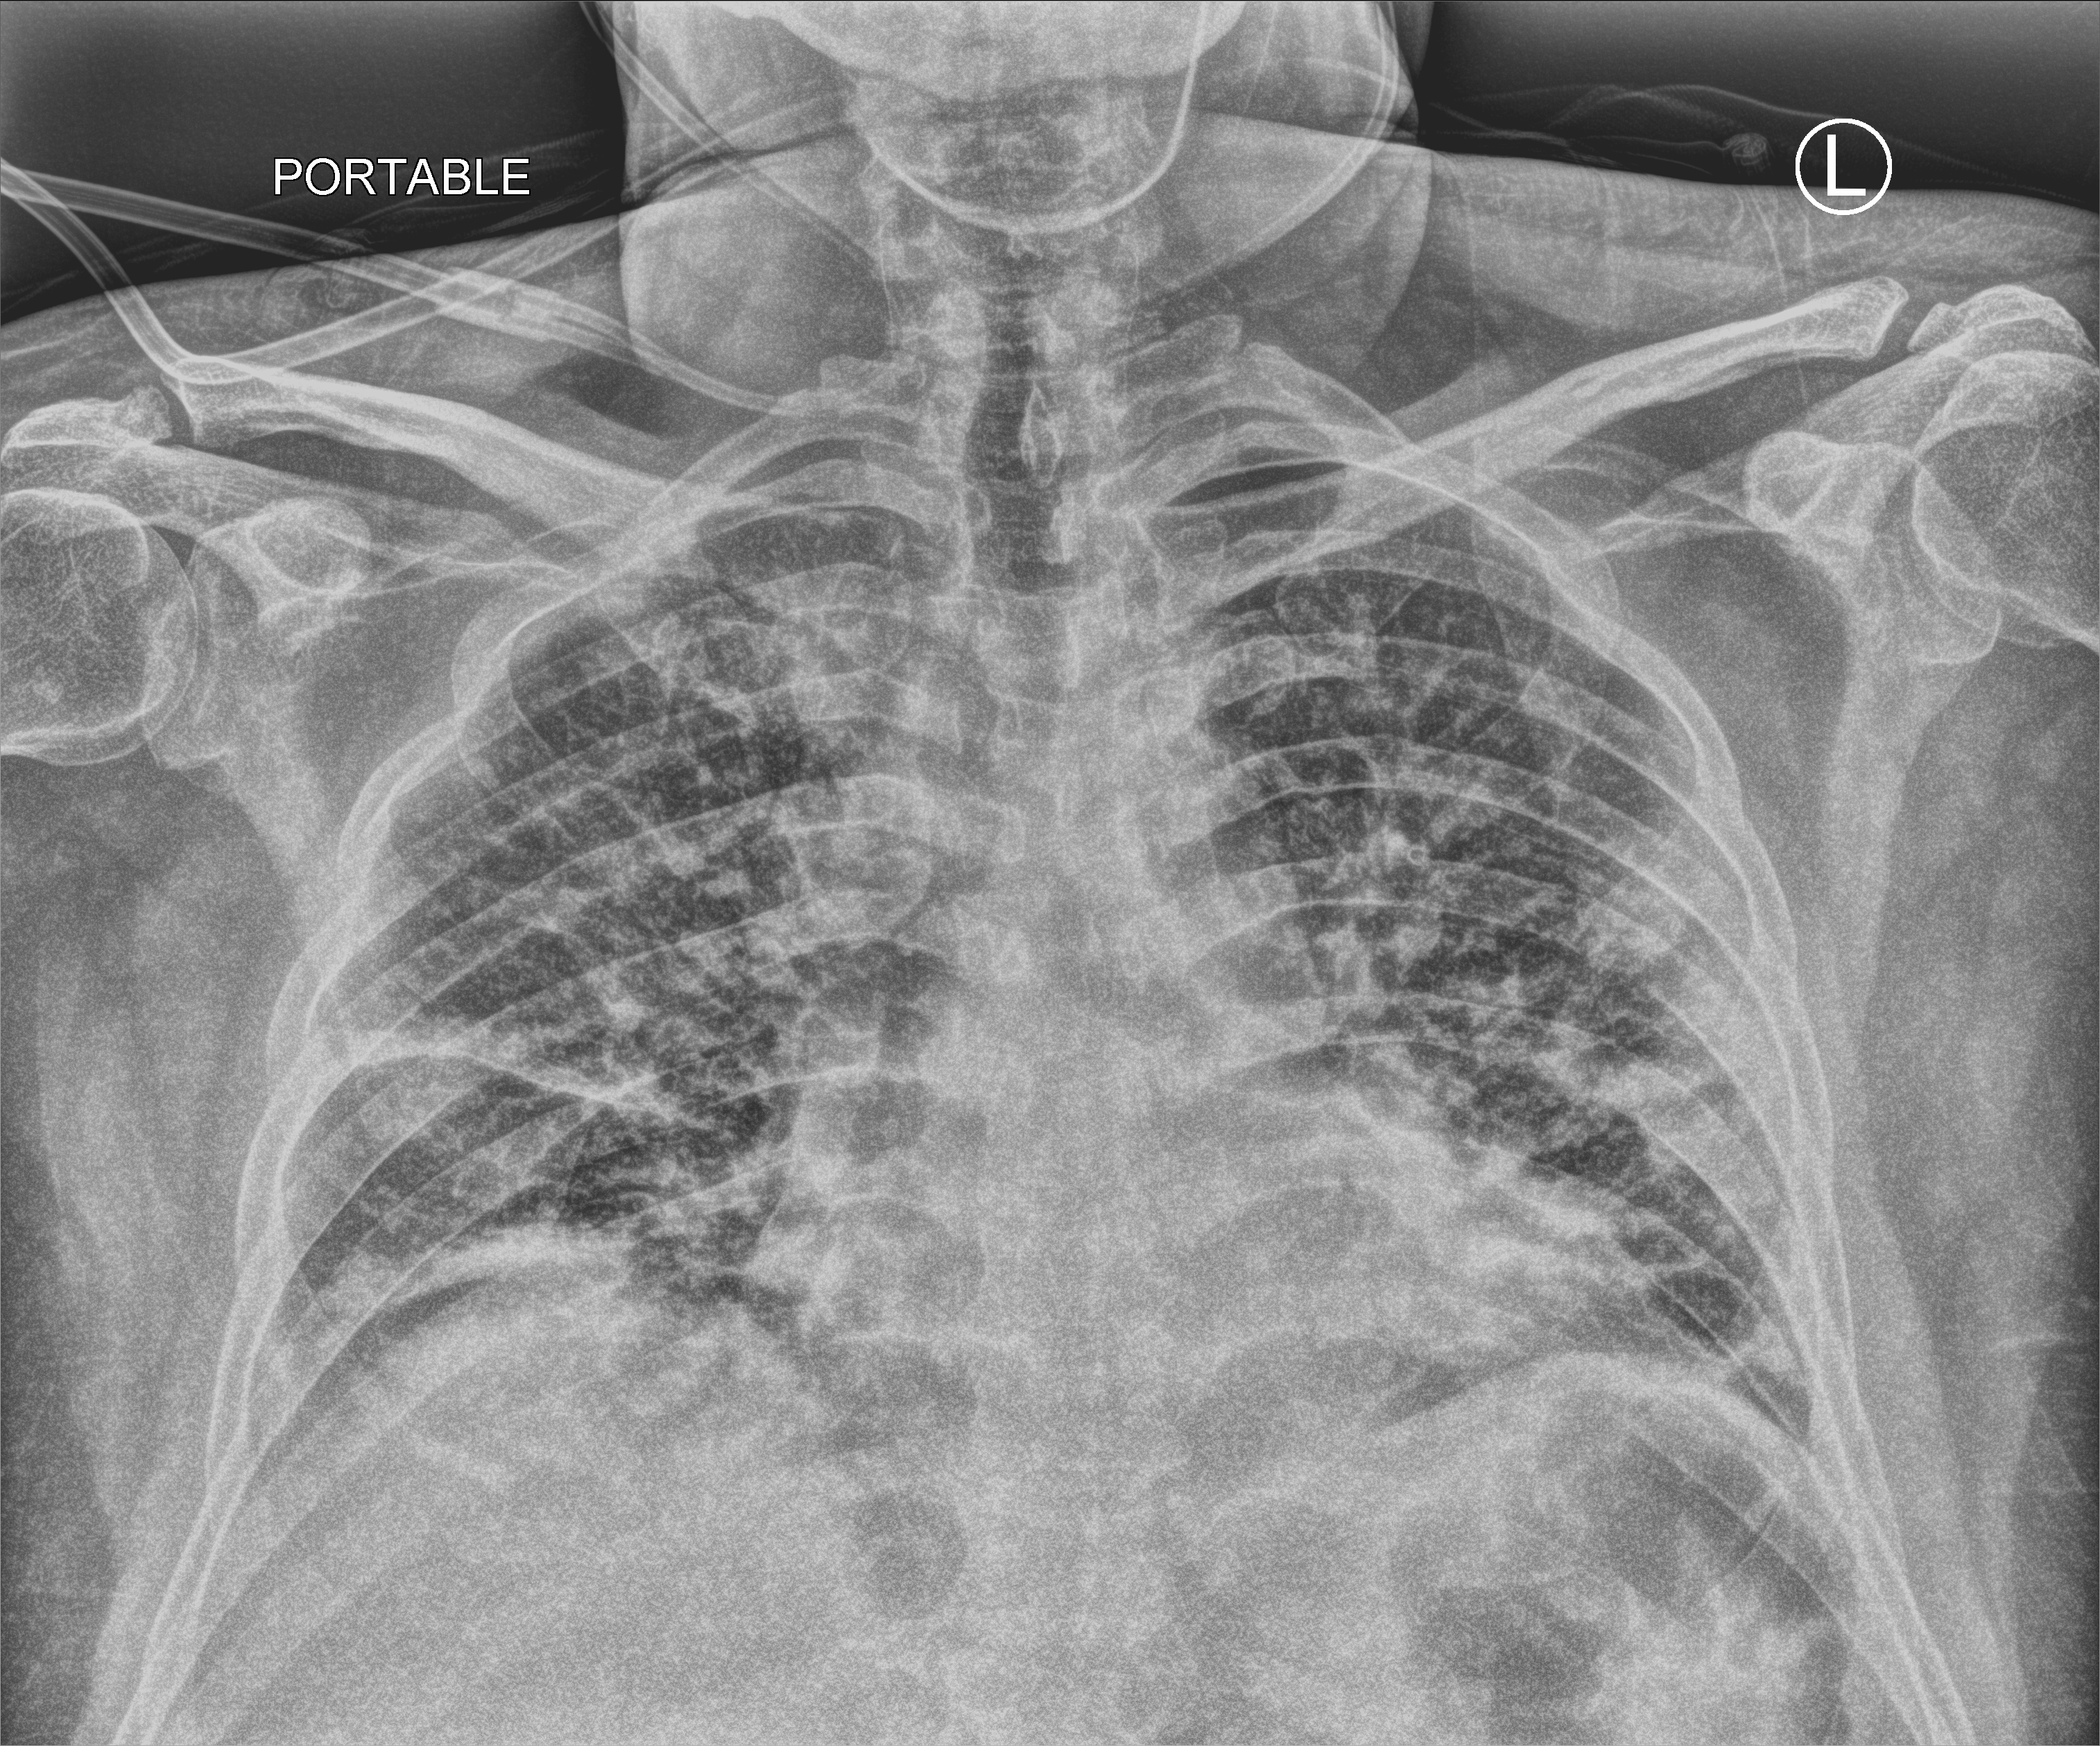
Chest X-ray (portable), anteroposterior (AP) projection. Patient hospitalised with COVID-19; male, aged 18–59 years.
From the hospital-stay record, not from the radiograph (when in the stay this image was taken is not recorded):
- admitted to intensive care during this hospital stay: no
- mechanically ventilated during this hospital stay: no